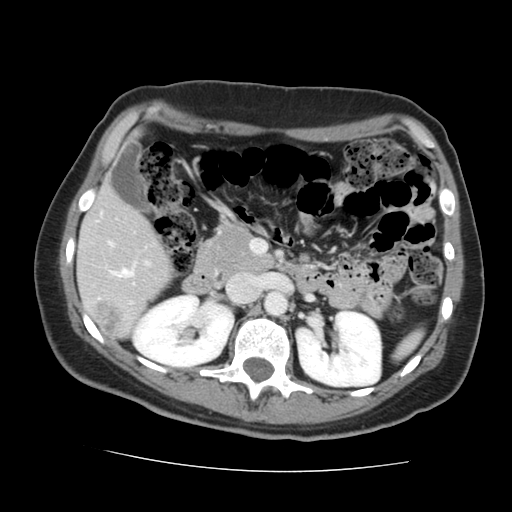
Contrast-enhanced abdominal CT, one axial slice. Position 74 of 144 along the scan axis. 120 kVp. Intravenous contrast given. Soft-tissue window (W 400 / L 40 HU). 2.5 mm slice thickness. 512 × 512 image matrix. Female patient, age 46 years. Case-level facts recorded for this patient, not image findings: diagnosis: colorectal cancer liver metastases, imaged before liver resection; multiple liver metastases: no; largest metastasis: 2.8 cm; disease in both lobes: no.
Annotated regions visible in this slice (manually delineated by an expert):
- liver: bounding box [x1, y1, x2, y2] px = [78, 187, 174, 338]
- planned liver remnant (the part of the liver to remain after resection): [78, 187, 174, 335]
- portal vein (with intrahepatic branches): [109, 242, 148, 278]
- liver metastasis: [97, 300, 120, 334]